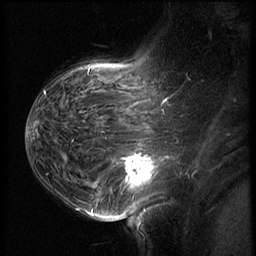
Breast MRI (dynamic contrast-enhanced), one sagittal slice; position 42 of 62 along the scan axis; 3 images stored at this slice position (order not interpretable as contrast timing); 1.5 T; TE 4.2 ms, TR 8.9 ms; 2.5 mm slice thickness; 256 × 256 image matrix, field of view 200 × 200 mm. Patient: female, 37 years. From the clinical record (not read from this slice): setting: breast cancer imaged before/during neoadjuvant chemotherapy; receptor status: triple-negative.
Annotated regions visible in this slice (semi-automatically segmented with operator editing):
- analysis volume of interest (the breast-tissue region the enhancement analysis was run in; not a lesion): bounding box [x1, y1, x2, y2] px = [116, 146, 168, 203]
- tumour enhancement mask (voxels above the 140 % enhancement threshold inside the analysis volume of interest): [123, 153, 156, 186]